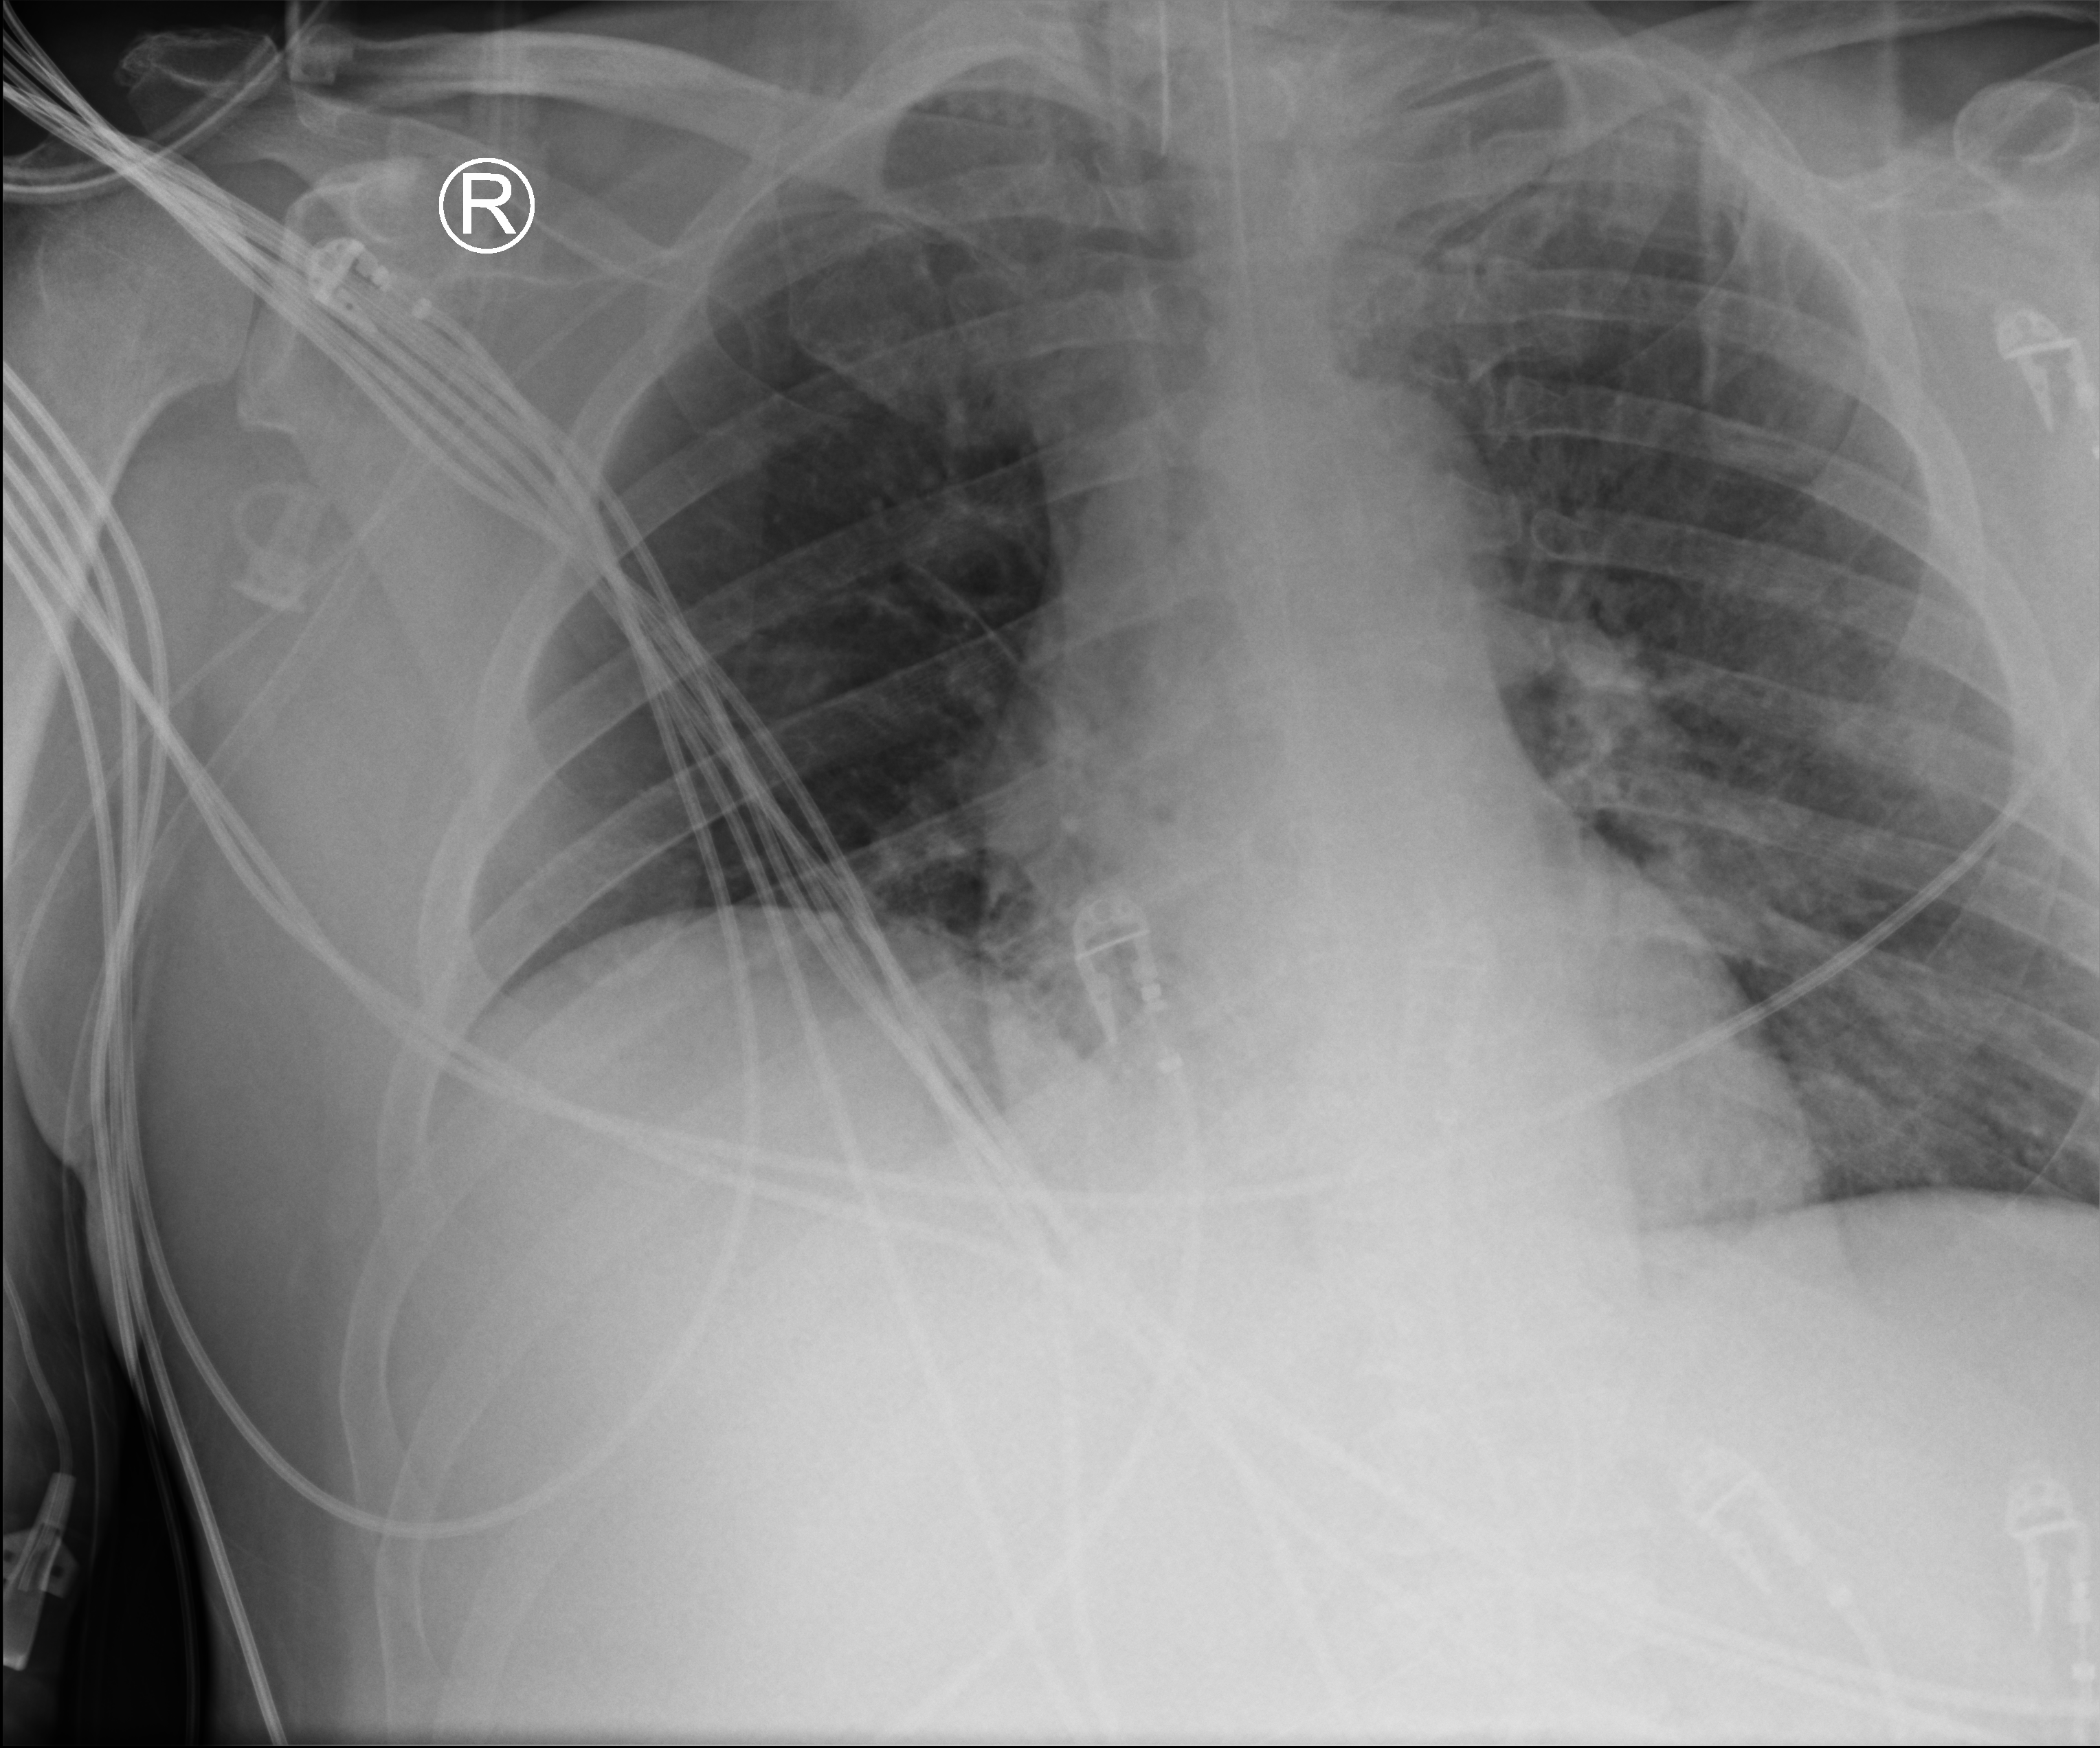
Chest X-ray (portable); anteroposterior (AP) projection. Patient hospitalised with COVID-19; male, aged 18–59 years.
Hospital-stay facts (about this admission, not read from this image; timing relative to this image not recorded):
- admitted to intensive care during this hospital stay: yes